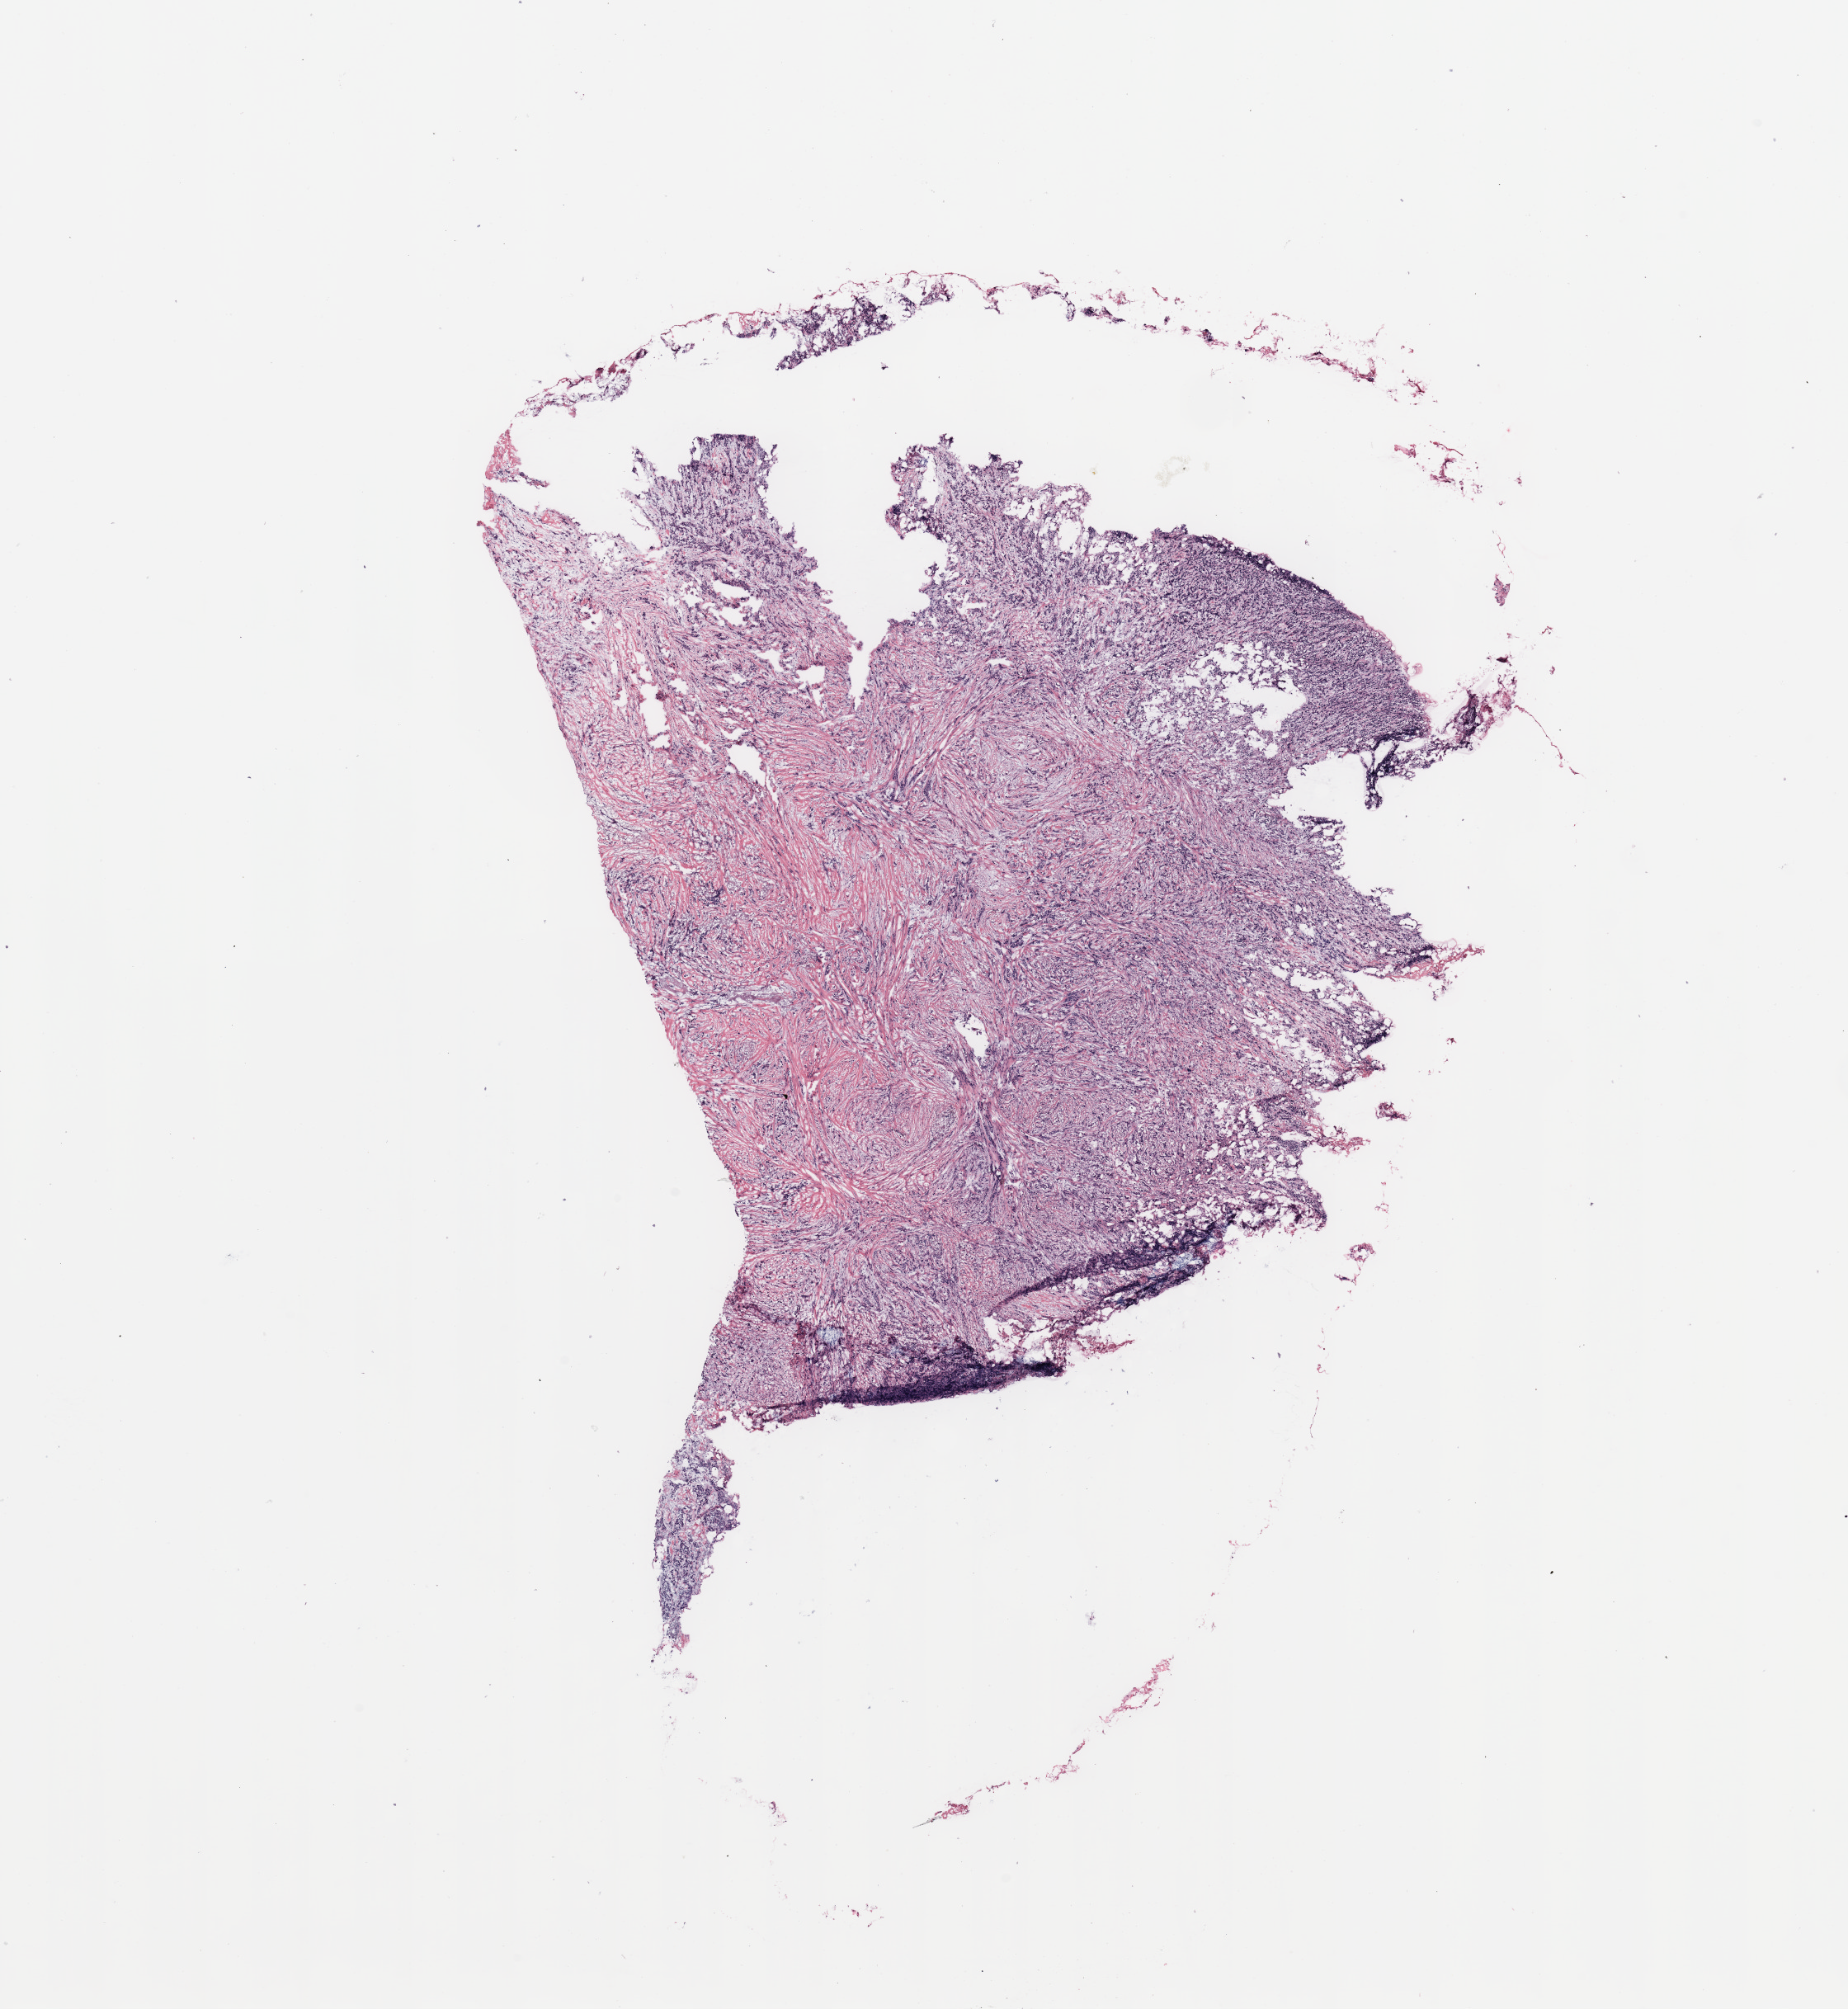
Hematoxylin and eosin (H&E) stained whole-slide image, a low-resolution overview of the entire scanned area, about 17.7 x 19.3 mm (from a 20x scan). Breast, tissue type not recorded.
* patient diagnosis (cohort enrolment): breast cancer (breast)